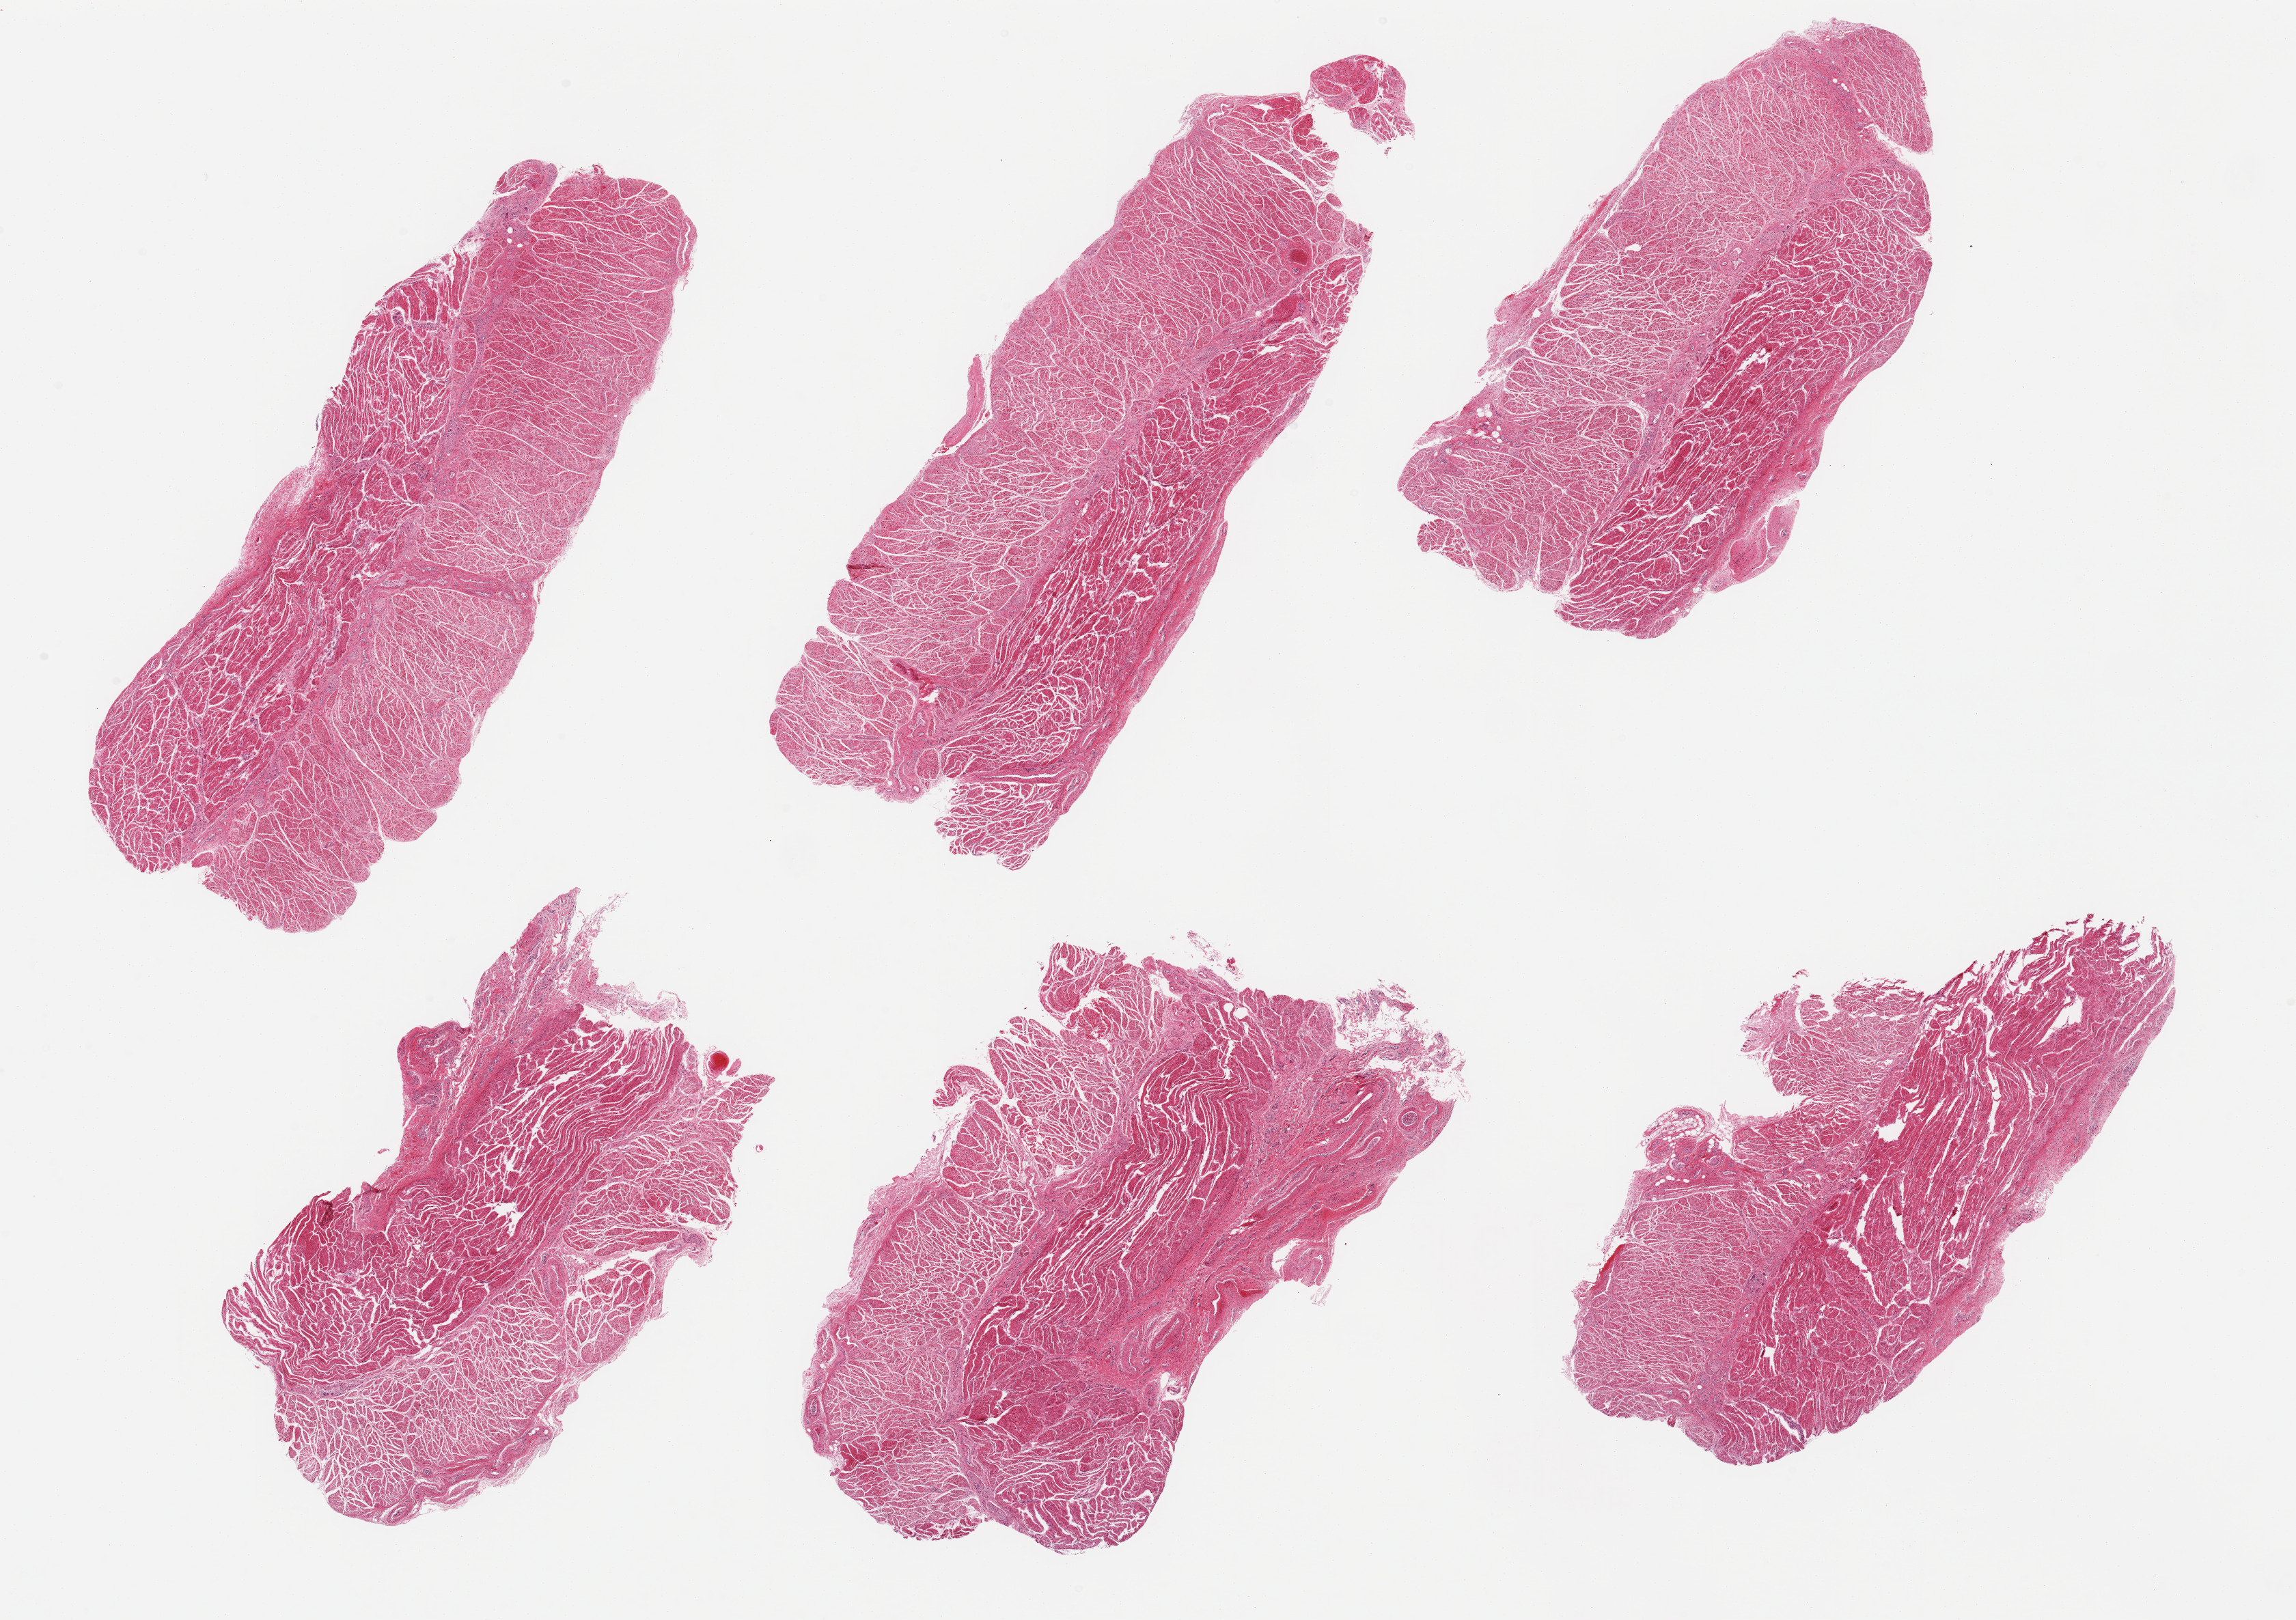
Digitized H&E-stained section, low-resolution overview of the scanned area, about 26.6 x 18.8 mm (slide scanned at 20x), PAXgene-fixed, paraffin-embedded tissue, target tissue: gastroesophageal junction, tissue donor sample.
Pathologist's review note for this sample: 6 pieces; well trimmed target muscularis.